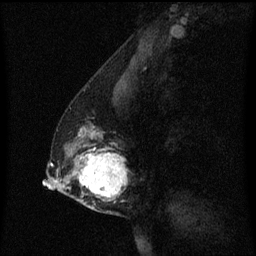
Breast MRI (dynamic contrast-enhanced), one sagittal slice. Slice 25 of 60 in the series (ordered by position). Dynamic contrast-enhanced series, image 2 of 3 at this slice position (ordered by acquisition). 1.5 T. TE 4.2 ms, TR 8.4 ms. 2 mm slice thickness. 256 × 256 image matrix, field of view 200 × 200 mm. Female patient, age 40 years. Case-level facts recorded for this patient, not image findings: setting: breast cancer imaged before/during neoadjuvant chemotherapy; receptor status: triple-negative.
Annotated regions visible in this slice (semi-automatic segmentation, software-assisted and operator-edited):
- analysis volume of interest (the breast-tissue region the enhancement analysis was run in; not a lesion): bounding box <60,112,131,215> (left, top, right, bottom; pixels)
- tumour enhancement mask (voxels above the 70 % enhancement threshold inside the analysis volume of interest): <80,130,129,201>